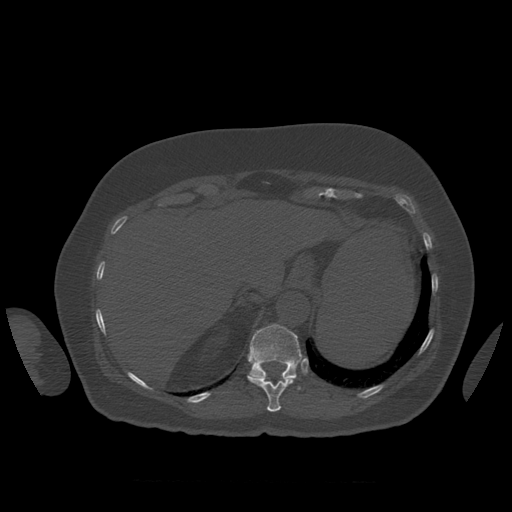
CT including the spine, one axial slice. Reconstruction kernel STANDARD. 120 kVp. Bone window (W 1800 / L 400 HU). 512 × 512 image matrix. Patient age 81 years. Case-level facts recorded for this patient, not image findings: primary cancer: renal; vertebrae with lytic lesions (as recorded): L1.
Outlined on this slice (semi-automatic segmentation, software-assisted and operator-edited):
- T11 vertebra: box from (x=247, y=376) to (x=294, y=412) px
- T12 vertebra: (x=248, y=324)–(x=303, y=390)